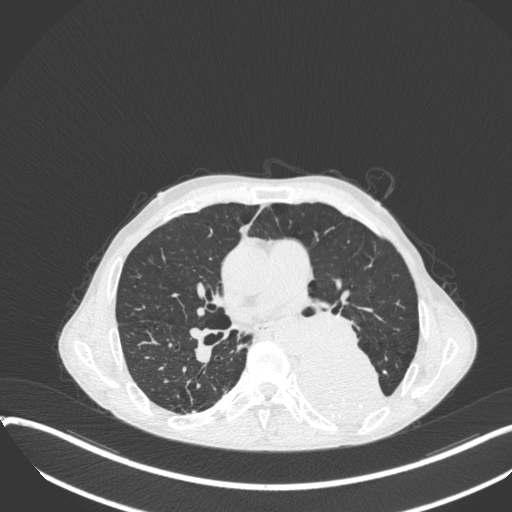
Chest CT, one axial slice; position 201 of 400 along the scan axis; reconstruction kernel B31f; lung window (W 1500 / L -600 HU); 1 mm slice thickness; 512 × 512 image matrix, field of view 400 × 400 mm. Patient: male, 57 years. From the clinical record (not read from this slice): clinical TNM (as recorded): T4 N0 M0.
Structures marked on this image (rectangle marked by the reading radiologist):
- lung tumour (recorded histology: squamous cell carcinoma): bounding box (x1, y1, x2, y2) in pixels: (294, 340, 390, 424)